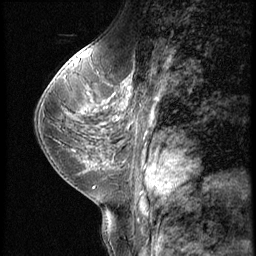
Breast MRI (dynamic contrast-enhanced), one sagittal slice. Position 29 of 56 along the scan axis. Dynamic contrast-enhanced series, image 2 of 3 at this slice position (ordered by acquisition). 1.5 T. TE 4.2 ms, TR 9 ms. 2.5 mm slice thickness. 256 × 256 image matrix, field of view 180 × 180 mm. Patient: female, 38 years. From the clinical record (not read from this slice): setting: breast cancer imaged before/during neoadjuvant chemotherapy; receptor status: triple-negative.
Annotated regions visible in this slice (semi-automatically segmented with operator editing):
- analysis volume of interest (the breast-tissue region the enhancement analysis was run in; not a lesion): box from (x=107, y=95) to (x=179, y=149) px
- tumour enhancement mask (voxels above the 140 % enhancement threshold inside the analysis volume of interest): (x=124, y=104)–(x=126, y=107)